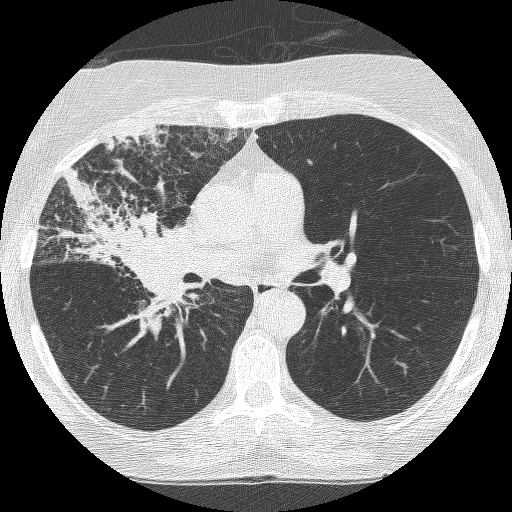
Chest CT (low-dose screening protocol), one axial image. Third screening round (two years after baseline). Lung window (W 1500 / L -600 HU). 1.25 mm slice thickness. Lung (sharp) reconstruction kernel (BONE). Slice 146 of 253 in the series. Female participant, aged 64 years at enrolment. Former smoker at enrolment.
Expert reader's lesion annotation, bounding box [x1, y1, x2, y2] px = [67, 181, 202, 318]. Screening reader's record for this exam (one nodule recorded; not confirmed to be the boxed lesion): non-calcified nodule or mass ≥4 mm, right upper lobe, 49 × 43 mm, spiculated (stellate) margins, soft tissue attenuation, pre-existing on the prior screen: yes; interval growth: yes.